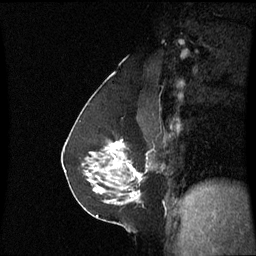
Breast MRI (dynamic contrast-enhanced), one sagittal slice; position 36 of 60 along the scan axis; dynamic contrast-enhanced series, image 2 of 3 at this slice position (ordered by acquisition); 1.5 T; TE 4.2 ms, TR 8.9 ms; 256 × 256 image matrix, field of view 220 × 220 mm. Patient: female, 58 years. From the clinical record (not read from this slice): setting: breast cancer imaged before/during neoadjuvant chemotherapy; receptor status: triple-negative.
Annotated regions visible in this slice (semi-automatically segmented with operator editing):
- analysis volume of interest (the breast-tissue region the enhancement analysis was run in; not a lesion): bounding box <90,140,149,193> (left, top, right, bottom; pixels)
- tumour enhancement mask (voxels above the 70 % enhancement threshold inside the analysis volume of interest): <90,142,135,179>